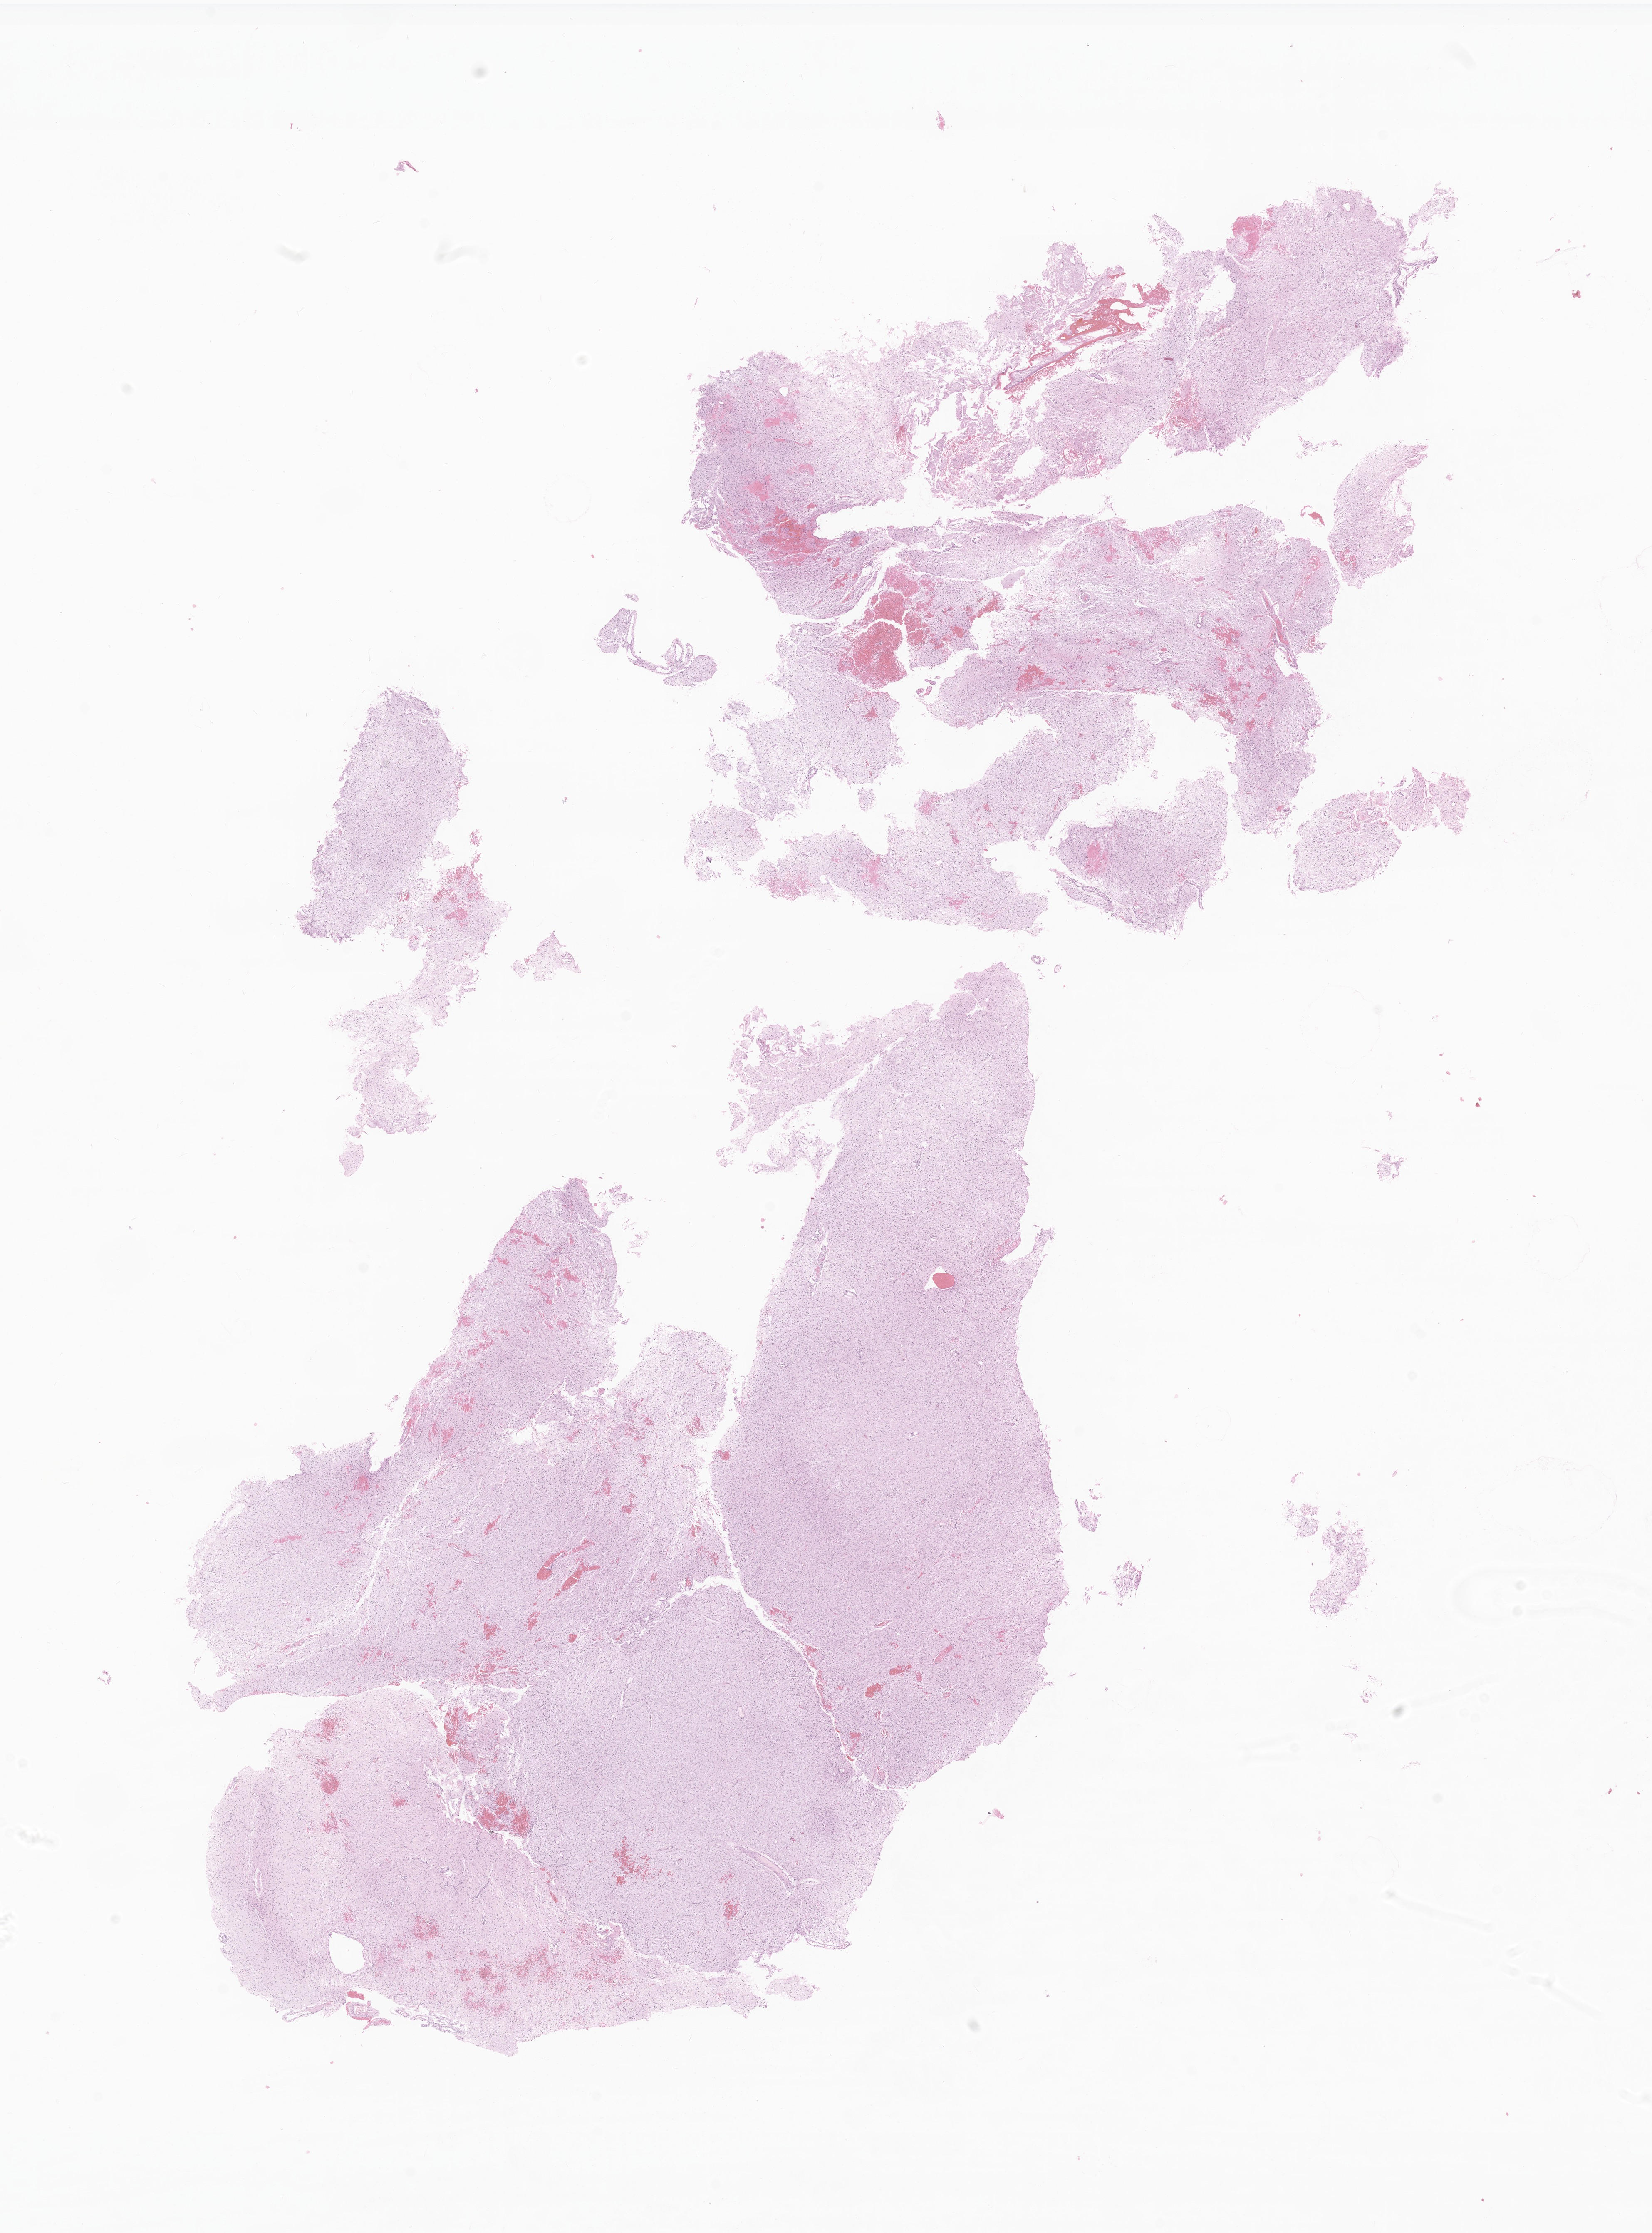
Whole-slide image, haematoxylin and eosin stain of tumor tissue from the brain stem, low-resolution overview of the scanned area, about 16.7 x 22.6 mm, formalin-fixed paraffin-embedded section. Patient female; age 173 months (14 years 5 months).
Diagnosis (ICD-O-3 morphology term): Astrocytoma, NOS.